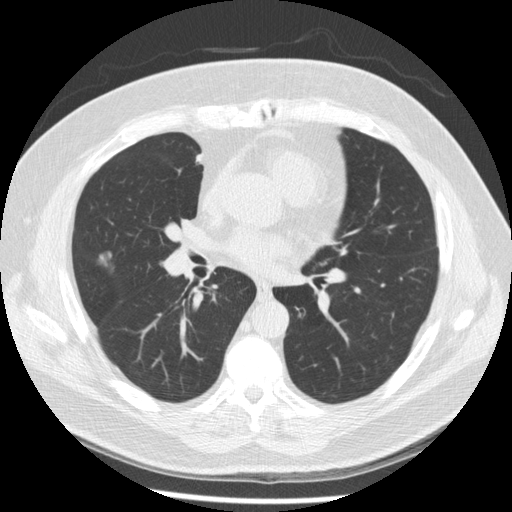
Low-dose screening chest CT, one axial slice; position 117 of 230 along the scan axis; reconstruction kernel STANDARD; 120 kVp; lung window (W 1500 / L -600 HU); 2.5 mm slice thickness; 512 × 512 image matrix, field of view 360 × 360 mm.
Annotated regions visible in this slice (expert manual segmentation):
- lesion 1 (tumor, middle lobe of right lung): box from (x=97, y=250) to (x=115, y=269) px